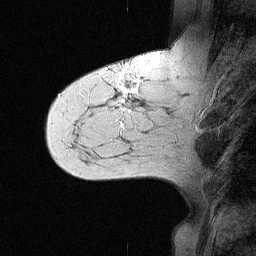
Breast MRI (dynamic contrast-enhanced), one sagittal slice. Position 19 of 64 along the scan axis. Dynamic contrast-enhanced study with each time point stored as its own series, time point 2 of 3 at this slice position (early post-contrast, ordered by acquisition time). 1.5 T. TE 4.5 ms, TR 11 ms. 256 × 256 image matrix. Patient: female, 55 years. From the clinical record (not read from this slice): setting: breast cancer imaged before/during neoadjuvant chemotherapy; receptor status: triple-negative.
Outlined on this slice (semi-automatically segmented with operator editing):
- analysis volume of interest (the breast-tissue region the enhancement analysis was run in; not a lesion): bounding box <71,63,147,145> (left, top, right, bottom; pixels)
- tumour enhancement mask (voxels above the 90 % enhancement threshold inside the analysis volume of interest): <106,70,139,126>